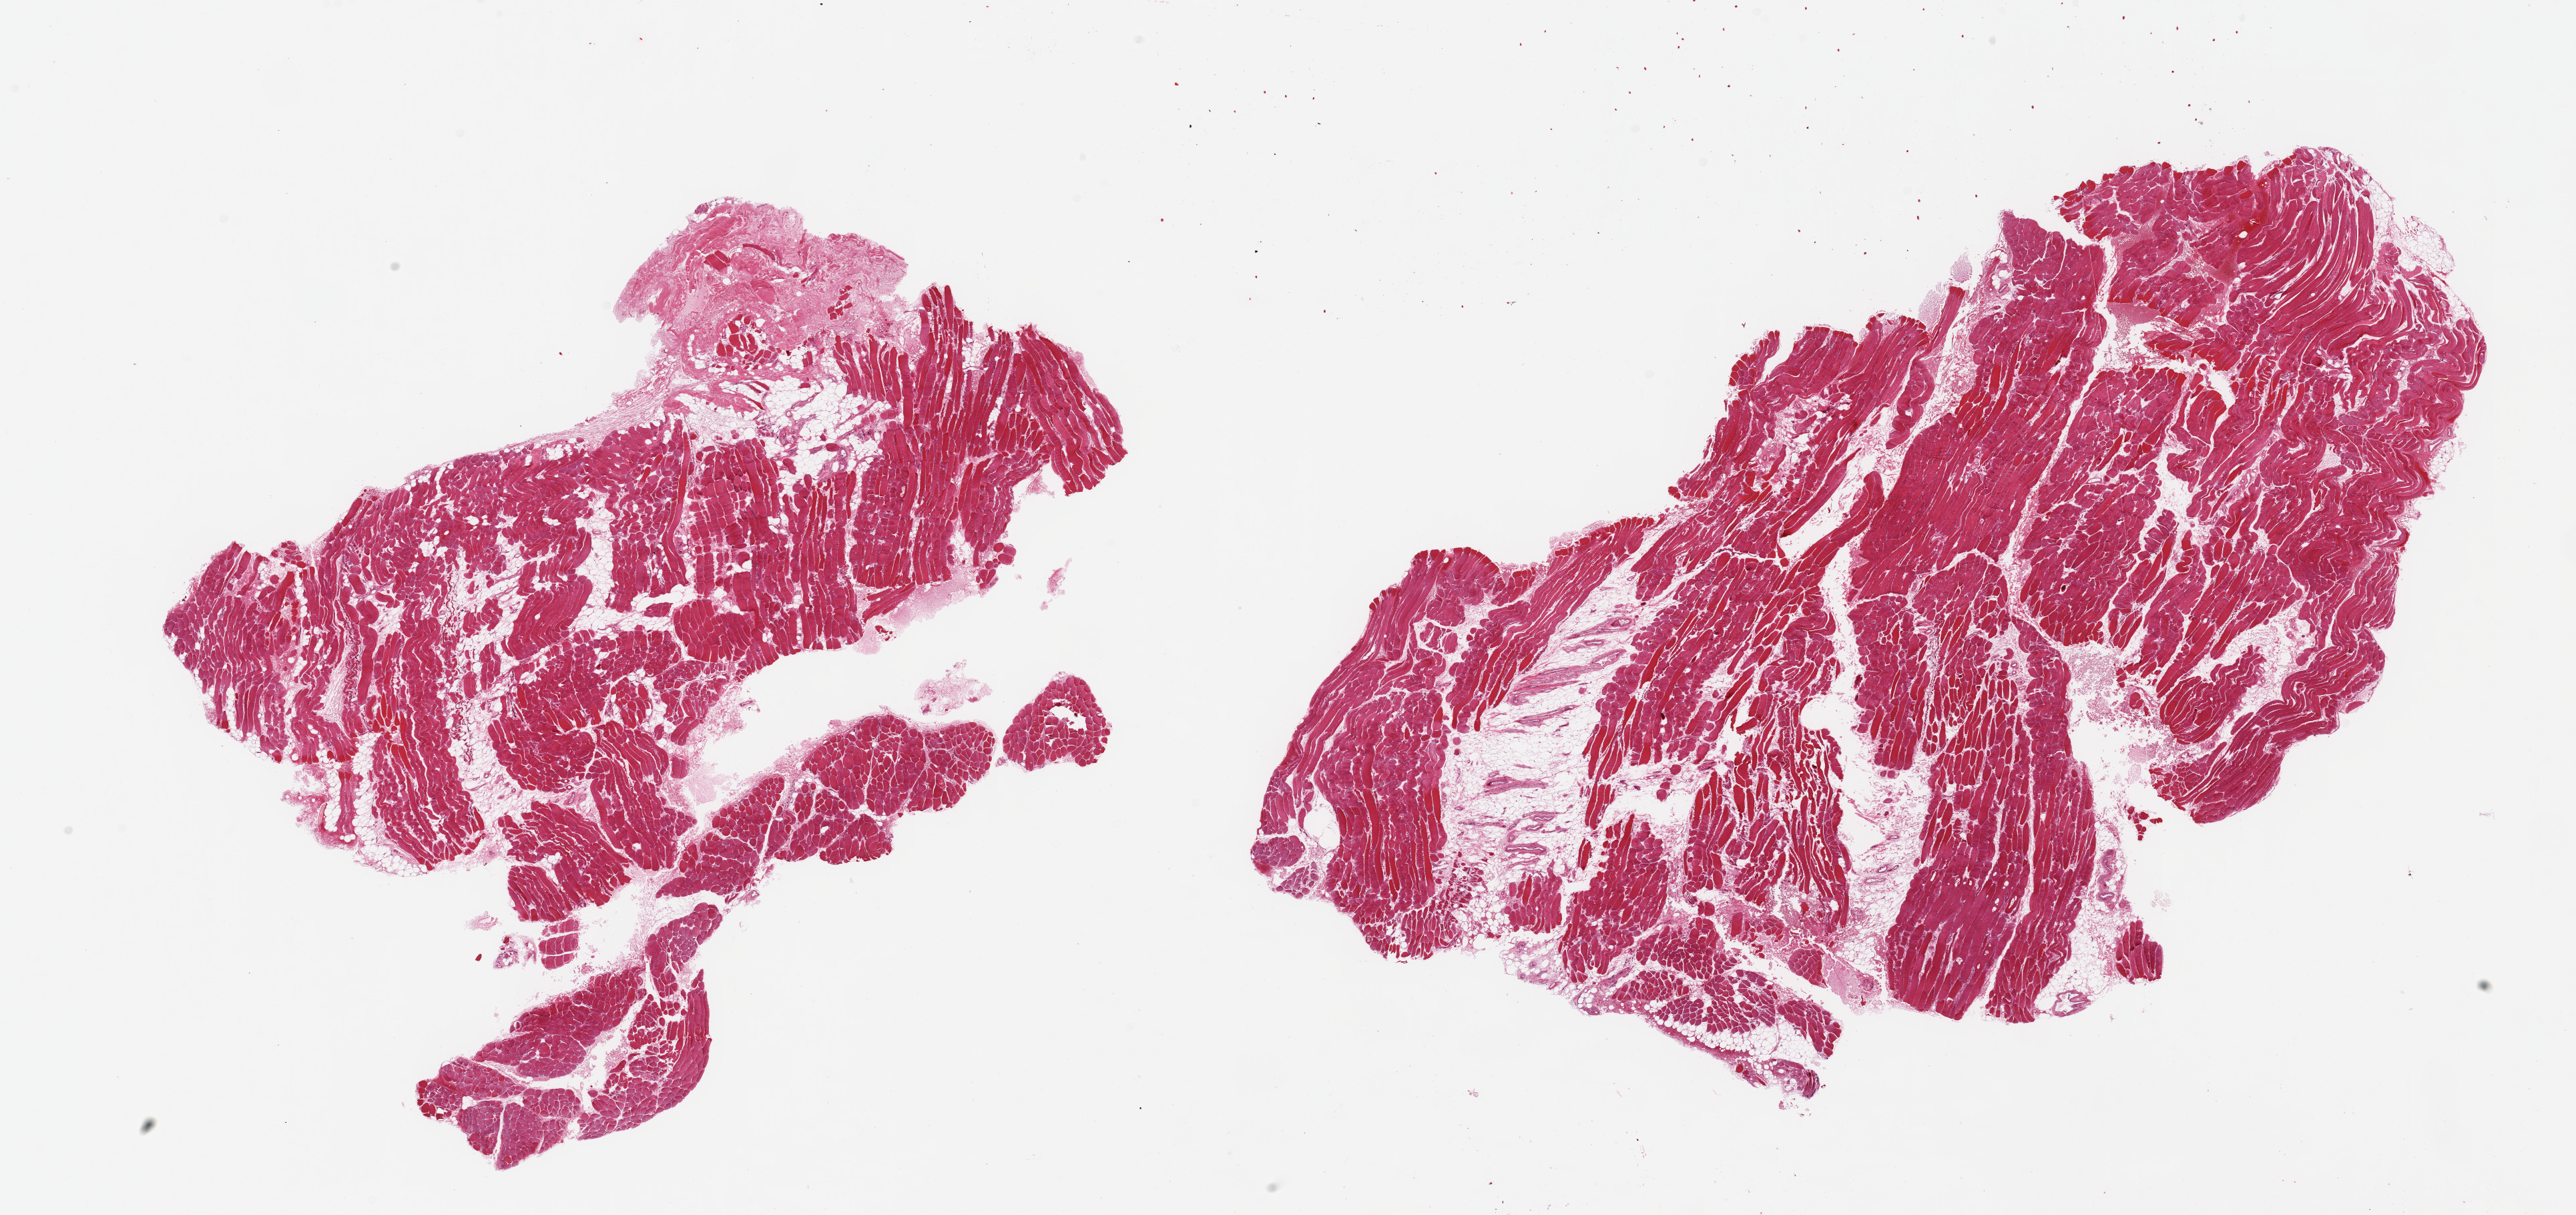
Haematoxylin and eosin whole-slide image — a low-resolution overview of the entire scanned area, about 30.5 x 14.4 mm. PAXgene-fixed, paraffin-embedded tissue. Target tissue: skeletal muscle. Tissue donor sample. Male donor.
Review note (as recorded): 2 pieces, ~20% interstitial fat/vascular elements; adherent tendon fragment.